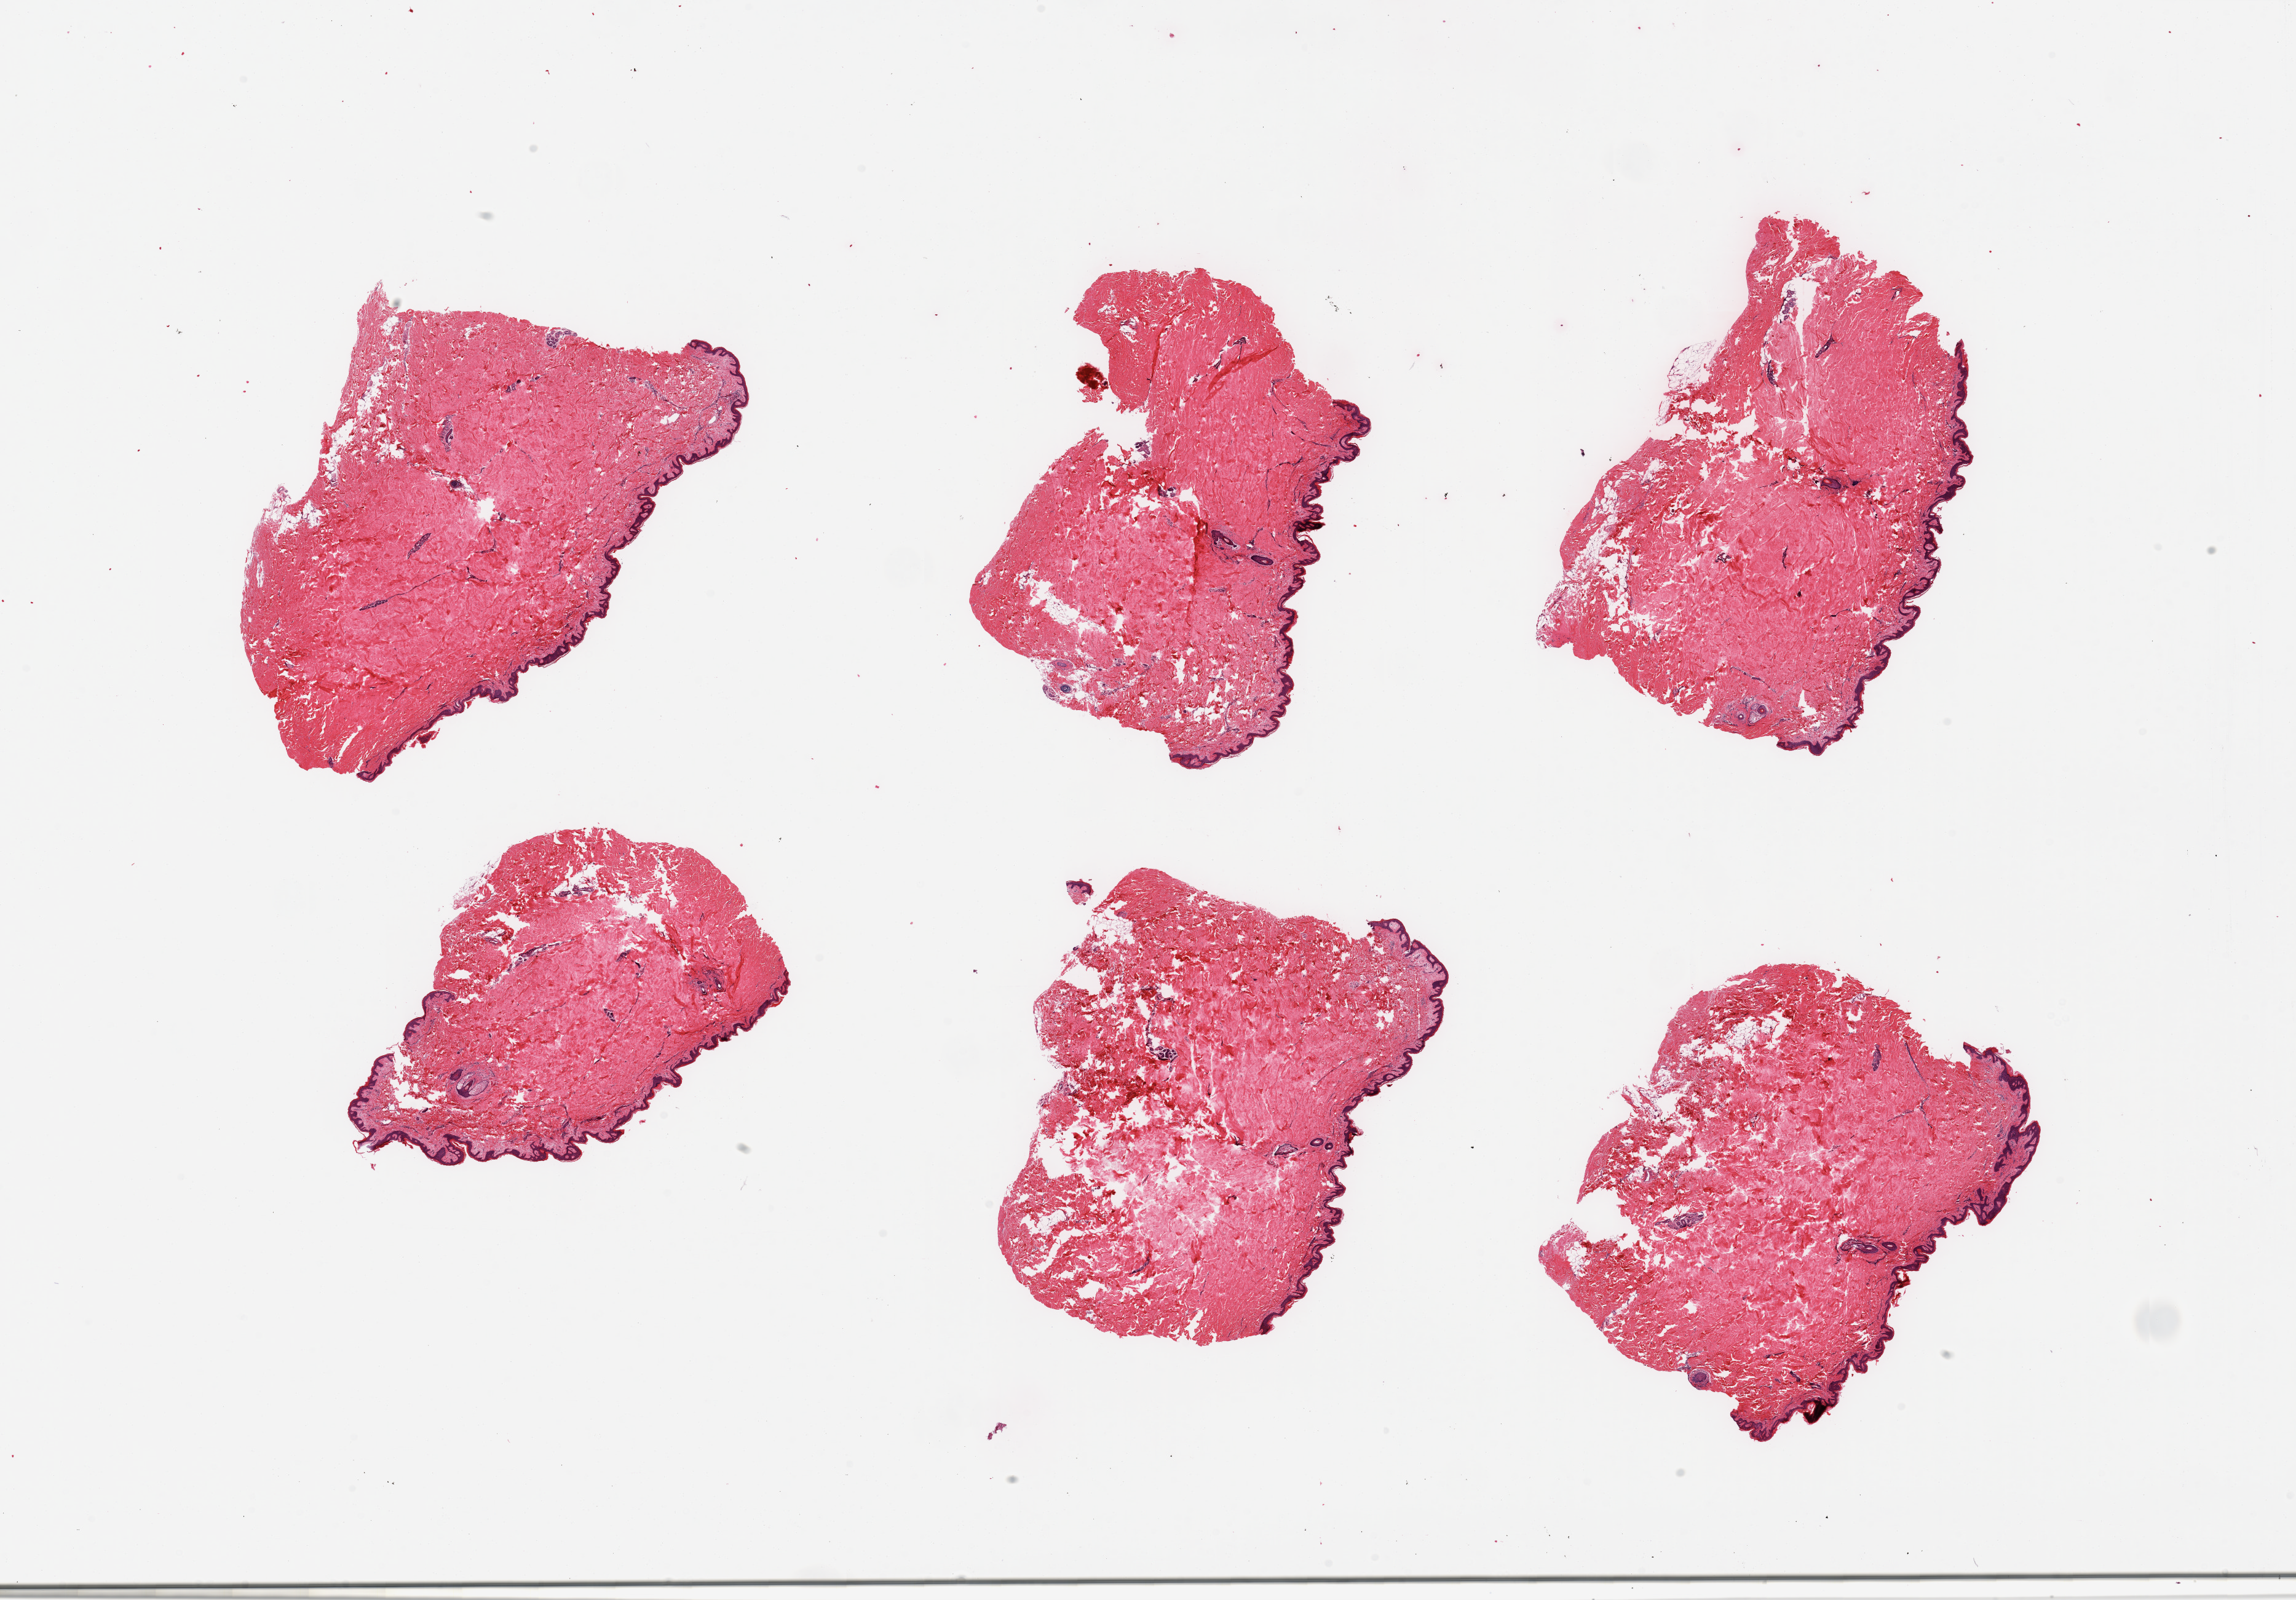
Haematoxylin and eosin whole-slide image, low-resolution overview of the scanned area, about 29.5 x 20.6 mm. PAXgene-fixed, paraffin-embedded tissue. Section of skin of suprapubic region (target tissue). Donor tissue sample. Male donor.
* reviewer comment on this tissue sample: 6 pieces; well trimmed